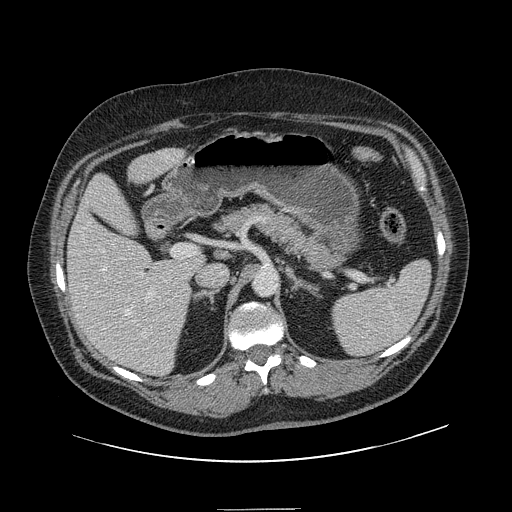
Contrast-enhanced abdominal CT, one axial slice; slice 81 of 154 in the series (ordered by position); intravenous contrast given; soft-tissue window (W 400 / L 40 HU); 512 × 512 image matrix, field of view 451 × 451 mm. Male patient, age 61 years. Case-level facts recorded for this patient, not image findings: diagnosis: colorectal cancer liver metastases, imaged before liver resection; multiple liver metastases: yes; largest metastasis: 2.6 cm; disease in both lobes: yes.
Outlined on this slice (outlined manually by an expert reader):
- hepatic veins: box from (x=102, y=266) to (x=152, y=337) px
- liver: (x=68, y=149)–(x=203, y=376)
- planned liver remnant (the part of the liver to remain after resection): (x=69, y=150)–(x=204, y=365)
- portal vein (with intrahepatic branches): (x=97, y=250)–(x=200, y=323)